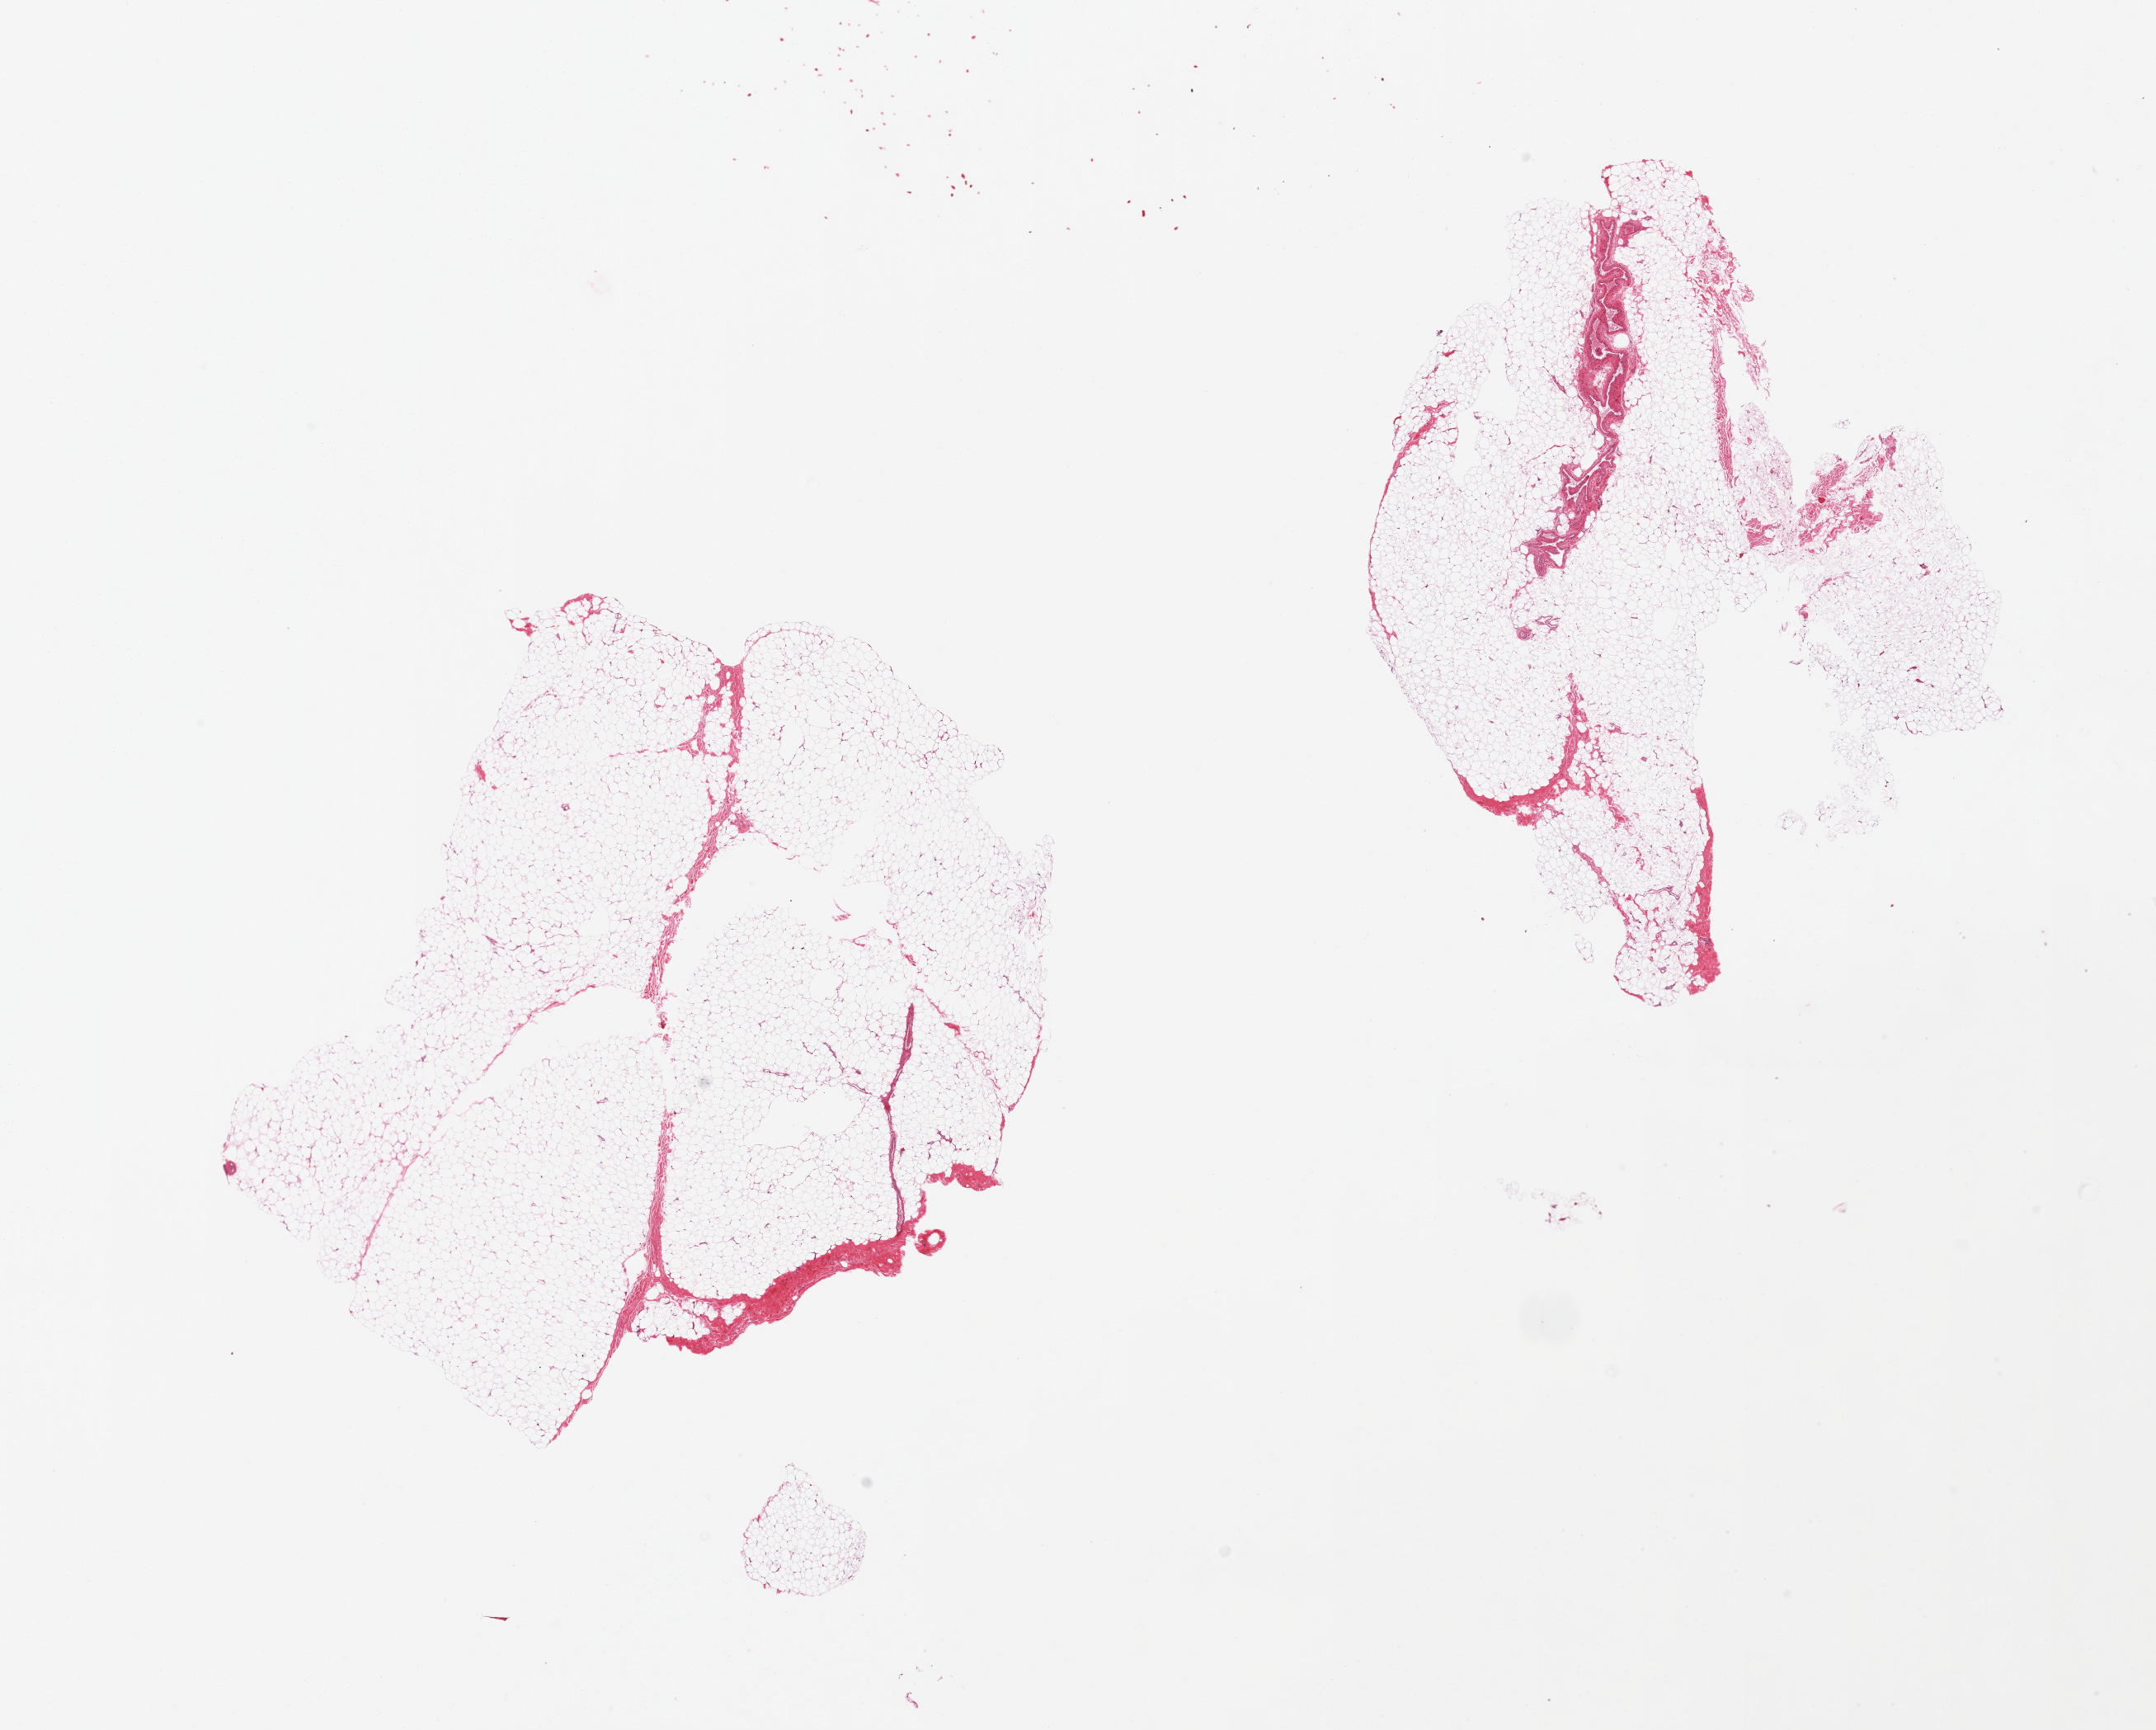
Whole-slide image, haematoxylin and eosin stain, brightfield — shown as a low-resolution overview of the whole scanned area (about 20.7 x 16.6 mm, acquisition: 20x scan); PAXgene-fixed paraffin-embedded (PFPE) section; sampled site (target tissue): breast; donor tissue sample. Male donor.
- reviewer comment on this tissue sample: 2 pieces; no mammary ducts, just fibroadipose tissue